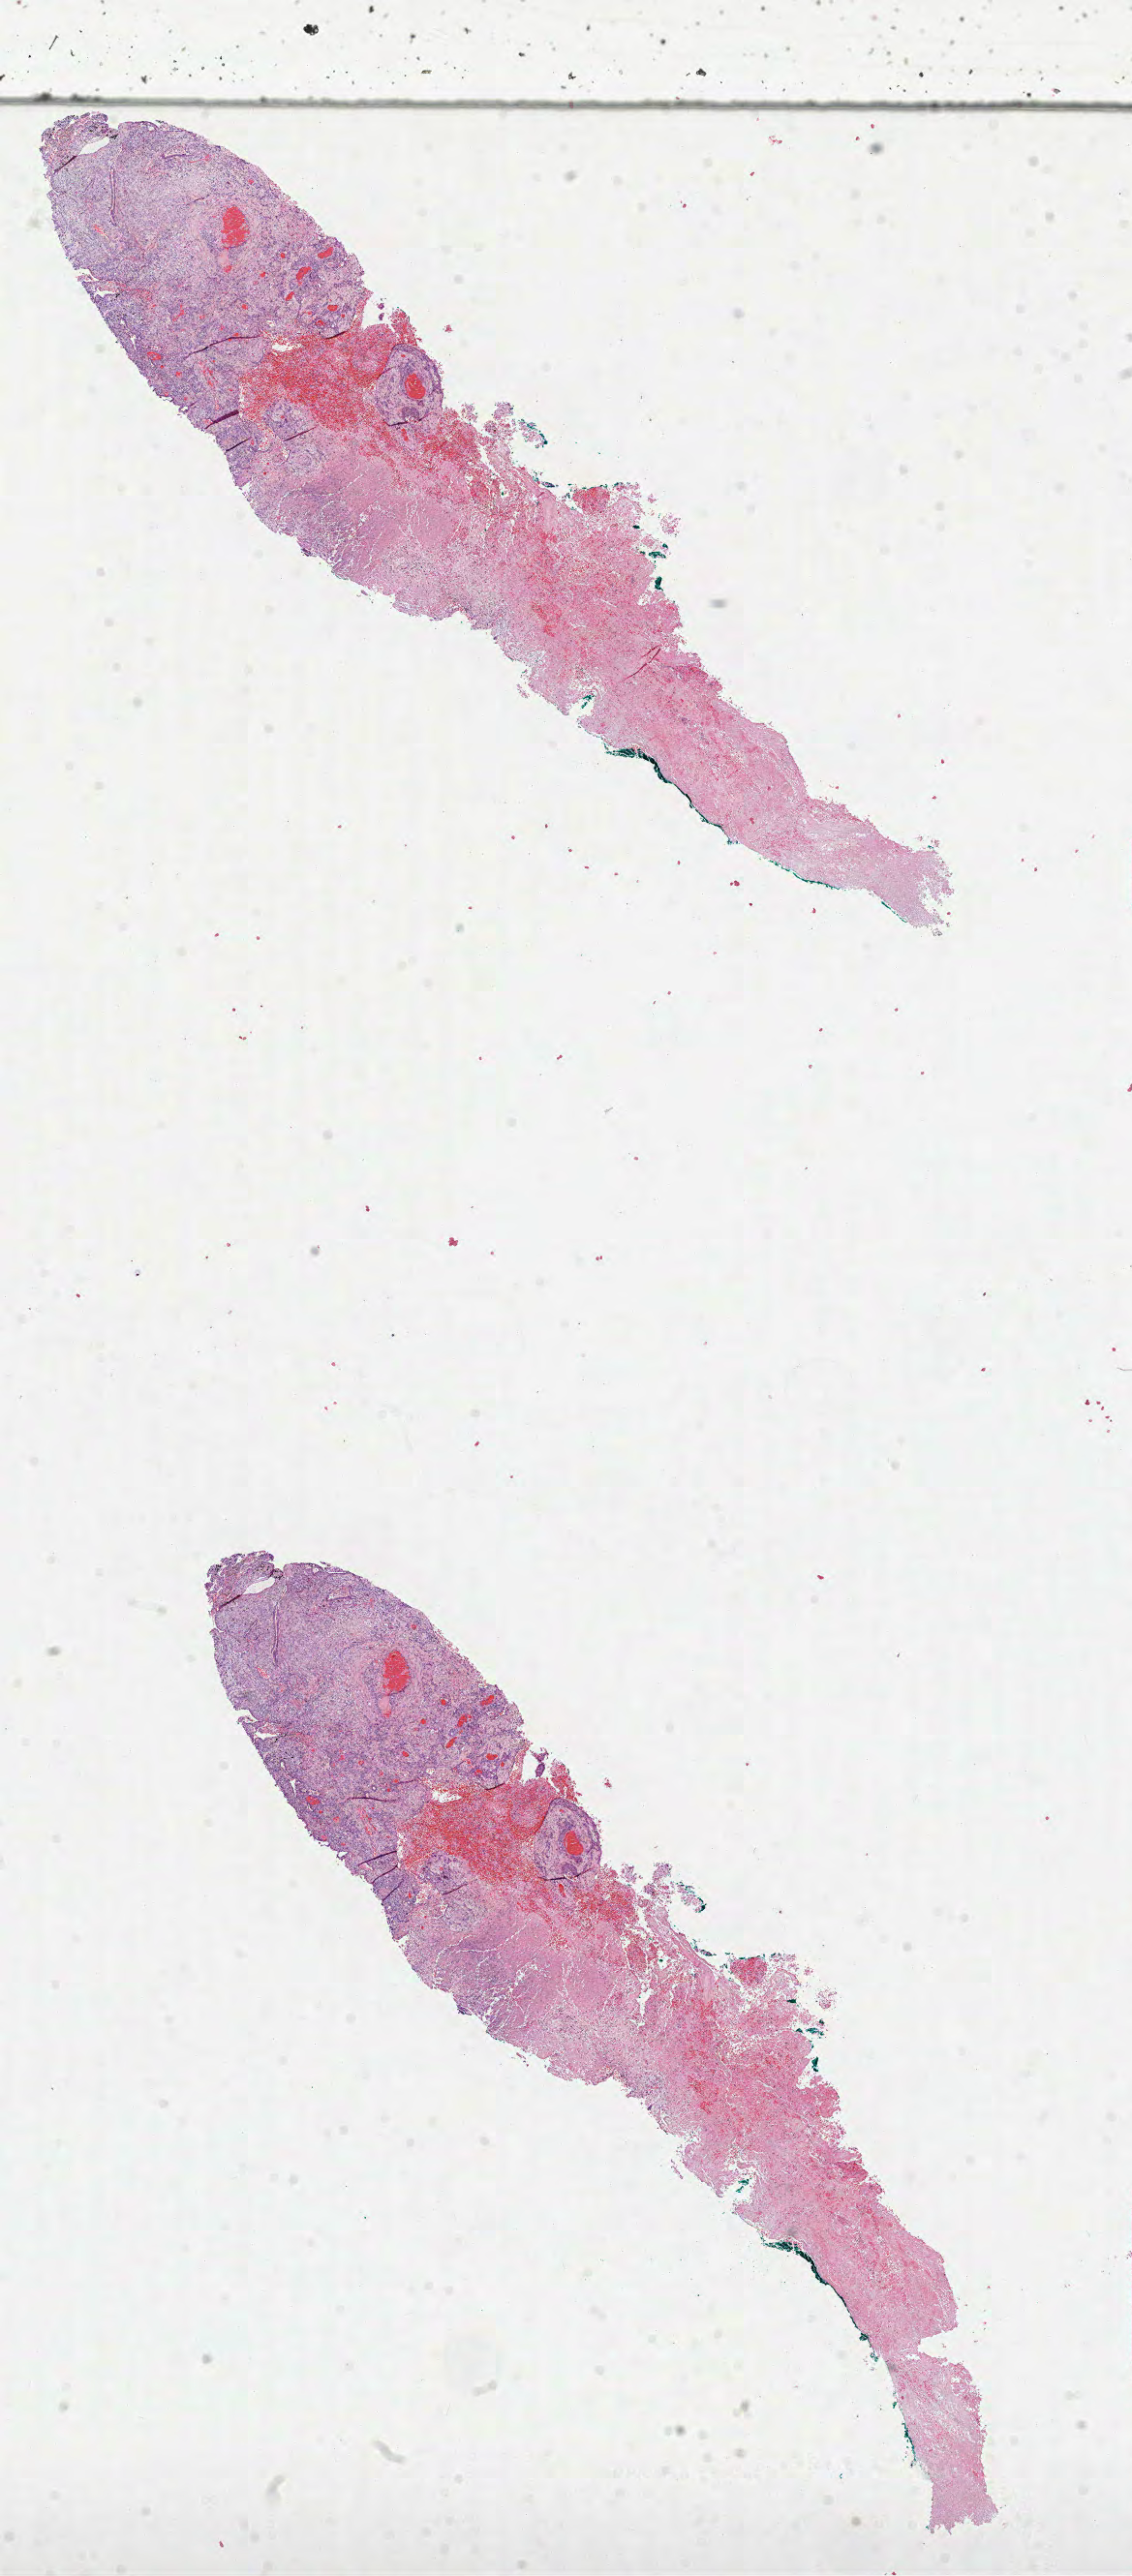
Whole-slide histology image, Hematoxylin and eosin (H&E) stained — low-resolution overview of the scanned area, about 9.4 x 21.5 mm. Formalin-fixed paraffin-embedded (FFPE) diagnostic section. Sample: primary tumour, lung. Patient: male, age at initial diagnosis 58 years.
AJCC pathologic stage: IB. Diagnosis: Squamous cell carcinoma, NOS.